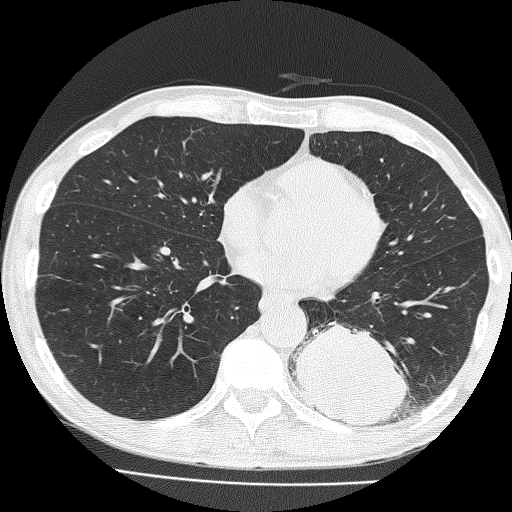
Low-dose screening chest CT, axial slice. Baseline annual screen. Lung window (W 1500 / L -600 HU). 2 mm slice thickness. 120 kVp. Slice 95 of 160 in the series. 512 × 512 image matrix. Male participant, aged 58 years at enrolment. Current smoker at enrolment.
Lesion marked by an expert reader, bounding box <297,305,423,434> (left, top, right, bottom; pixels). The screening reader recorded 2 non-calcified nodules or masses ≥4 mm on this exam (left lower lobe, left upper lobe); which of them this box marks is not recorded.